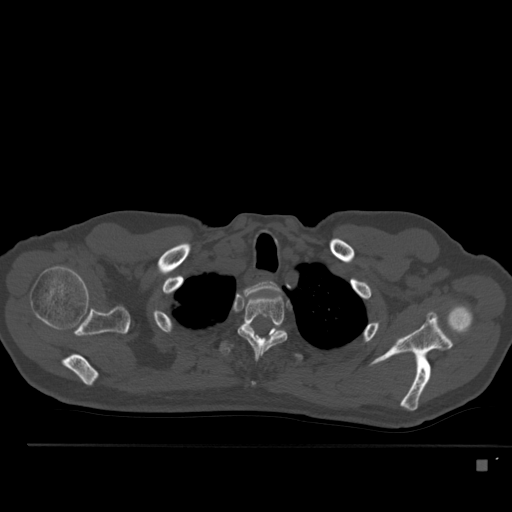
CT including the spine, one axial slice; slice 410 of 517 in the series (ordered by position); reconstruction kernel Br40s; 120 kVp; bone window (W 1800 / L 400 HU); 1.5 mm slice thickness; 512 × 512 image matrix. Patient: male, 70 years. From the clinical record (not read from this slice): primary cancer: renal.
Structures marked on this image (semi-automatic segmentation, software-assisted and operator-edited):
- T1 vertebra: box from (x=245, y=281) to (x=279, y=294) px
- T2 vertebra: (x=237, y=294)–(x=288, y=358)
- T3 vertebra: (x=219, y=323)–(x=303, y=361)